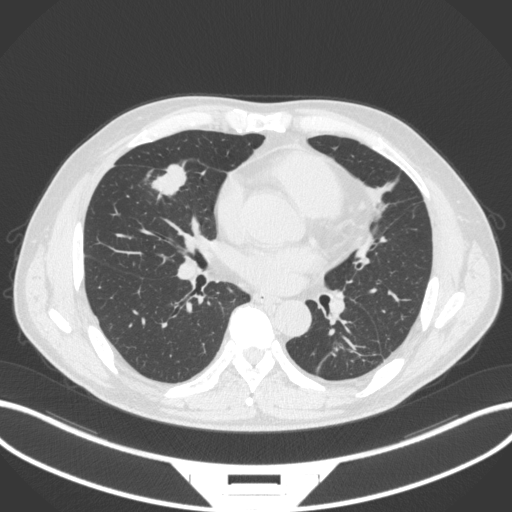
Chest CT, one axial slice. Position 145 of 399 along the scan axis. 120 kVp. Lung window (W 1500 / L -600 HU). 1 mm slice thickness. 512 × 512 image matrix. Male patient, age 59 years. Case-level facts recorded for this patient, not image findings: clinical TNM (as recorded): T2a N1 M0.
Structures marked on this image (bounding box drawn by a radiologist):
- lung tumour (recorded histology: adenocarcinoma): box from (x=150, y=160) to (x=190, y=197) px